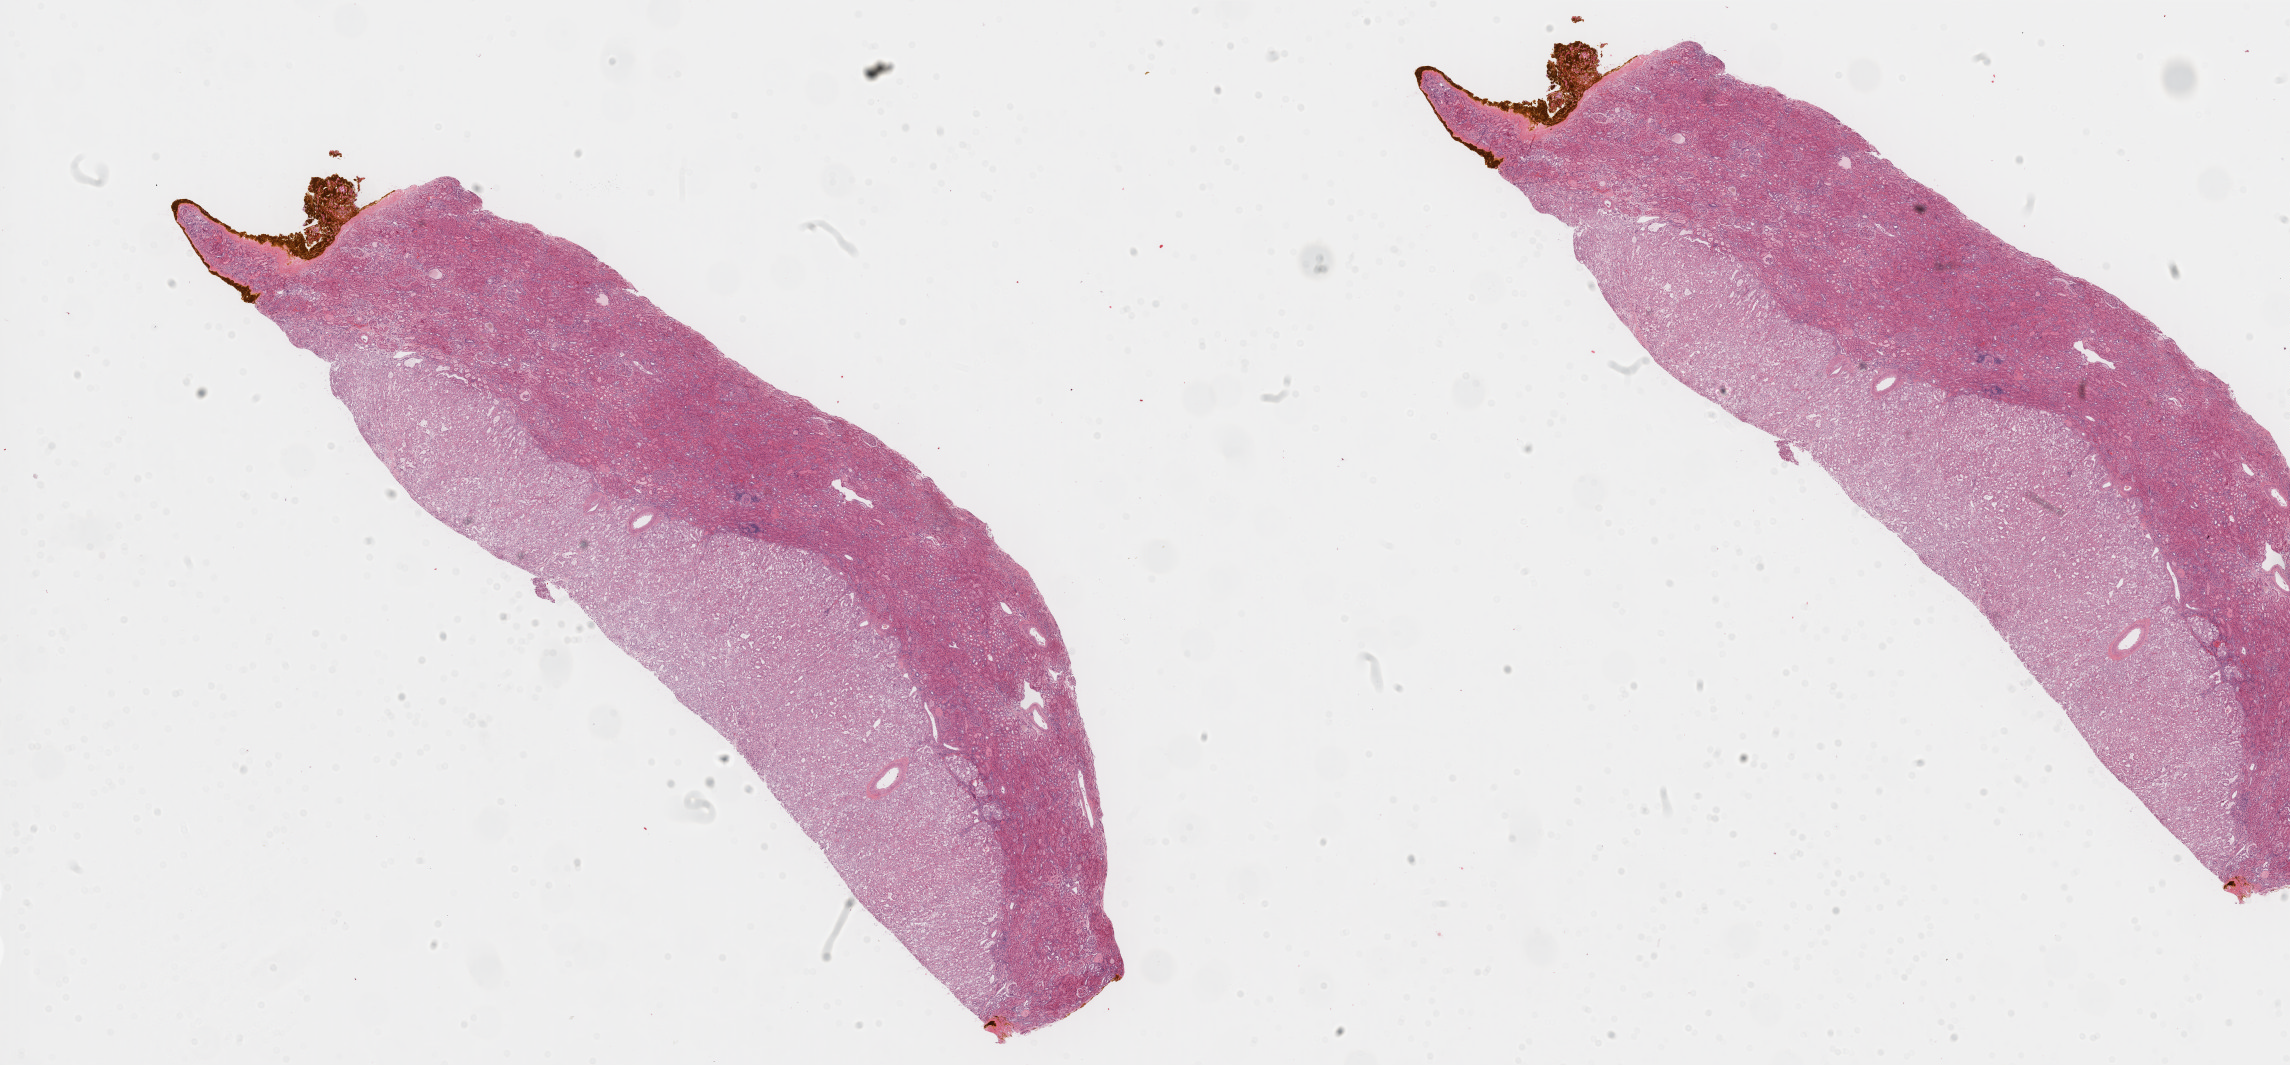
Whole-slide histology image, Hematoxylin and eosin (H&E) stained — shown as a low-resolution overview of the whole scanned area (about 36.2 x 16.9 mm, from a 40x scan). Formalin-fixed paraffin-embedded (FFPE) diagnostic section. Primary tumour sample from the kidney. Female patient; age at initial diagnosis 51 years.
- AJCC pathologic stage: I (7th edition)
- pathologic diagnosis: Renal cell carcinoma, chromophobe type